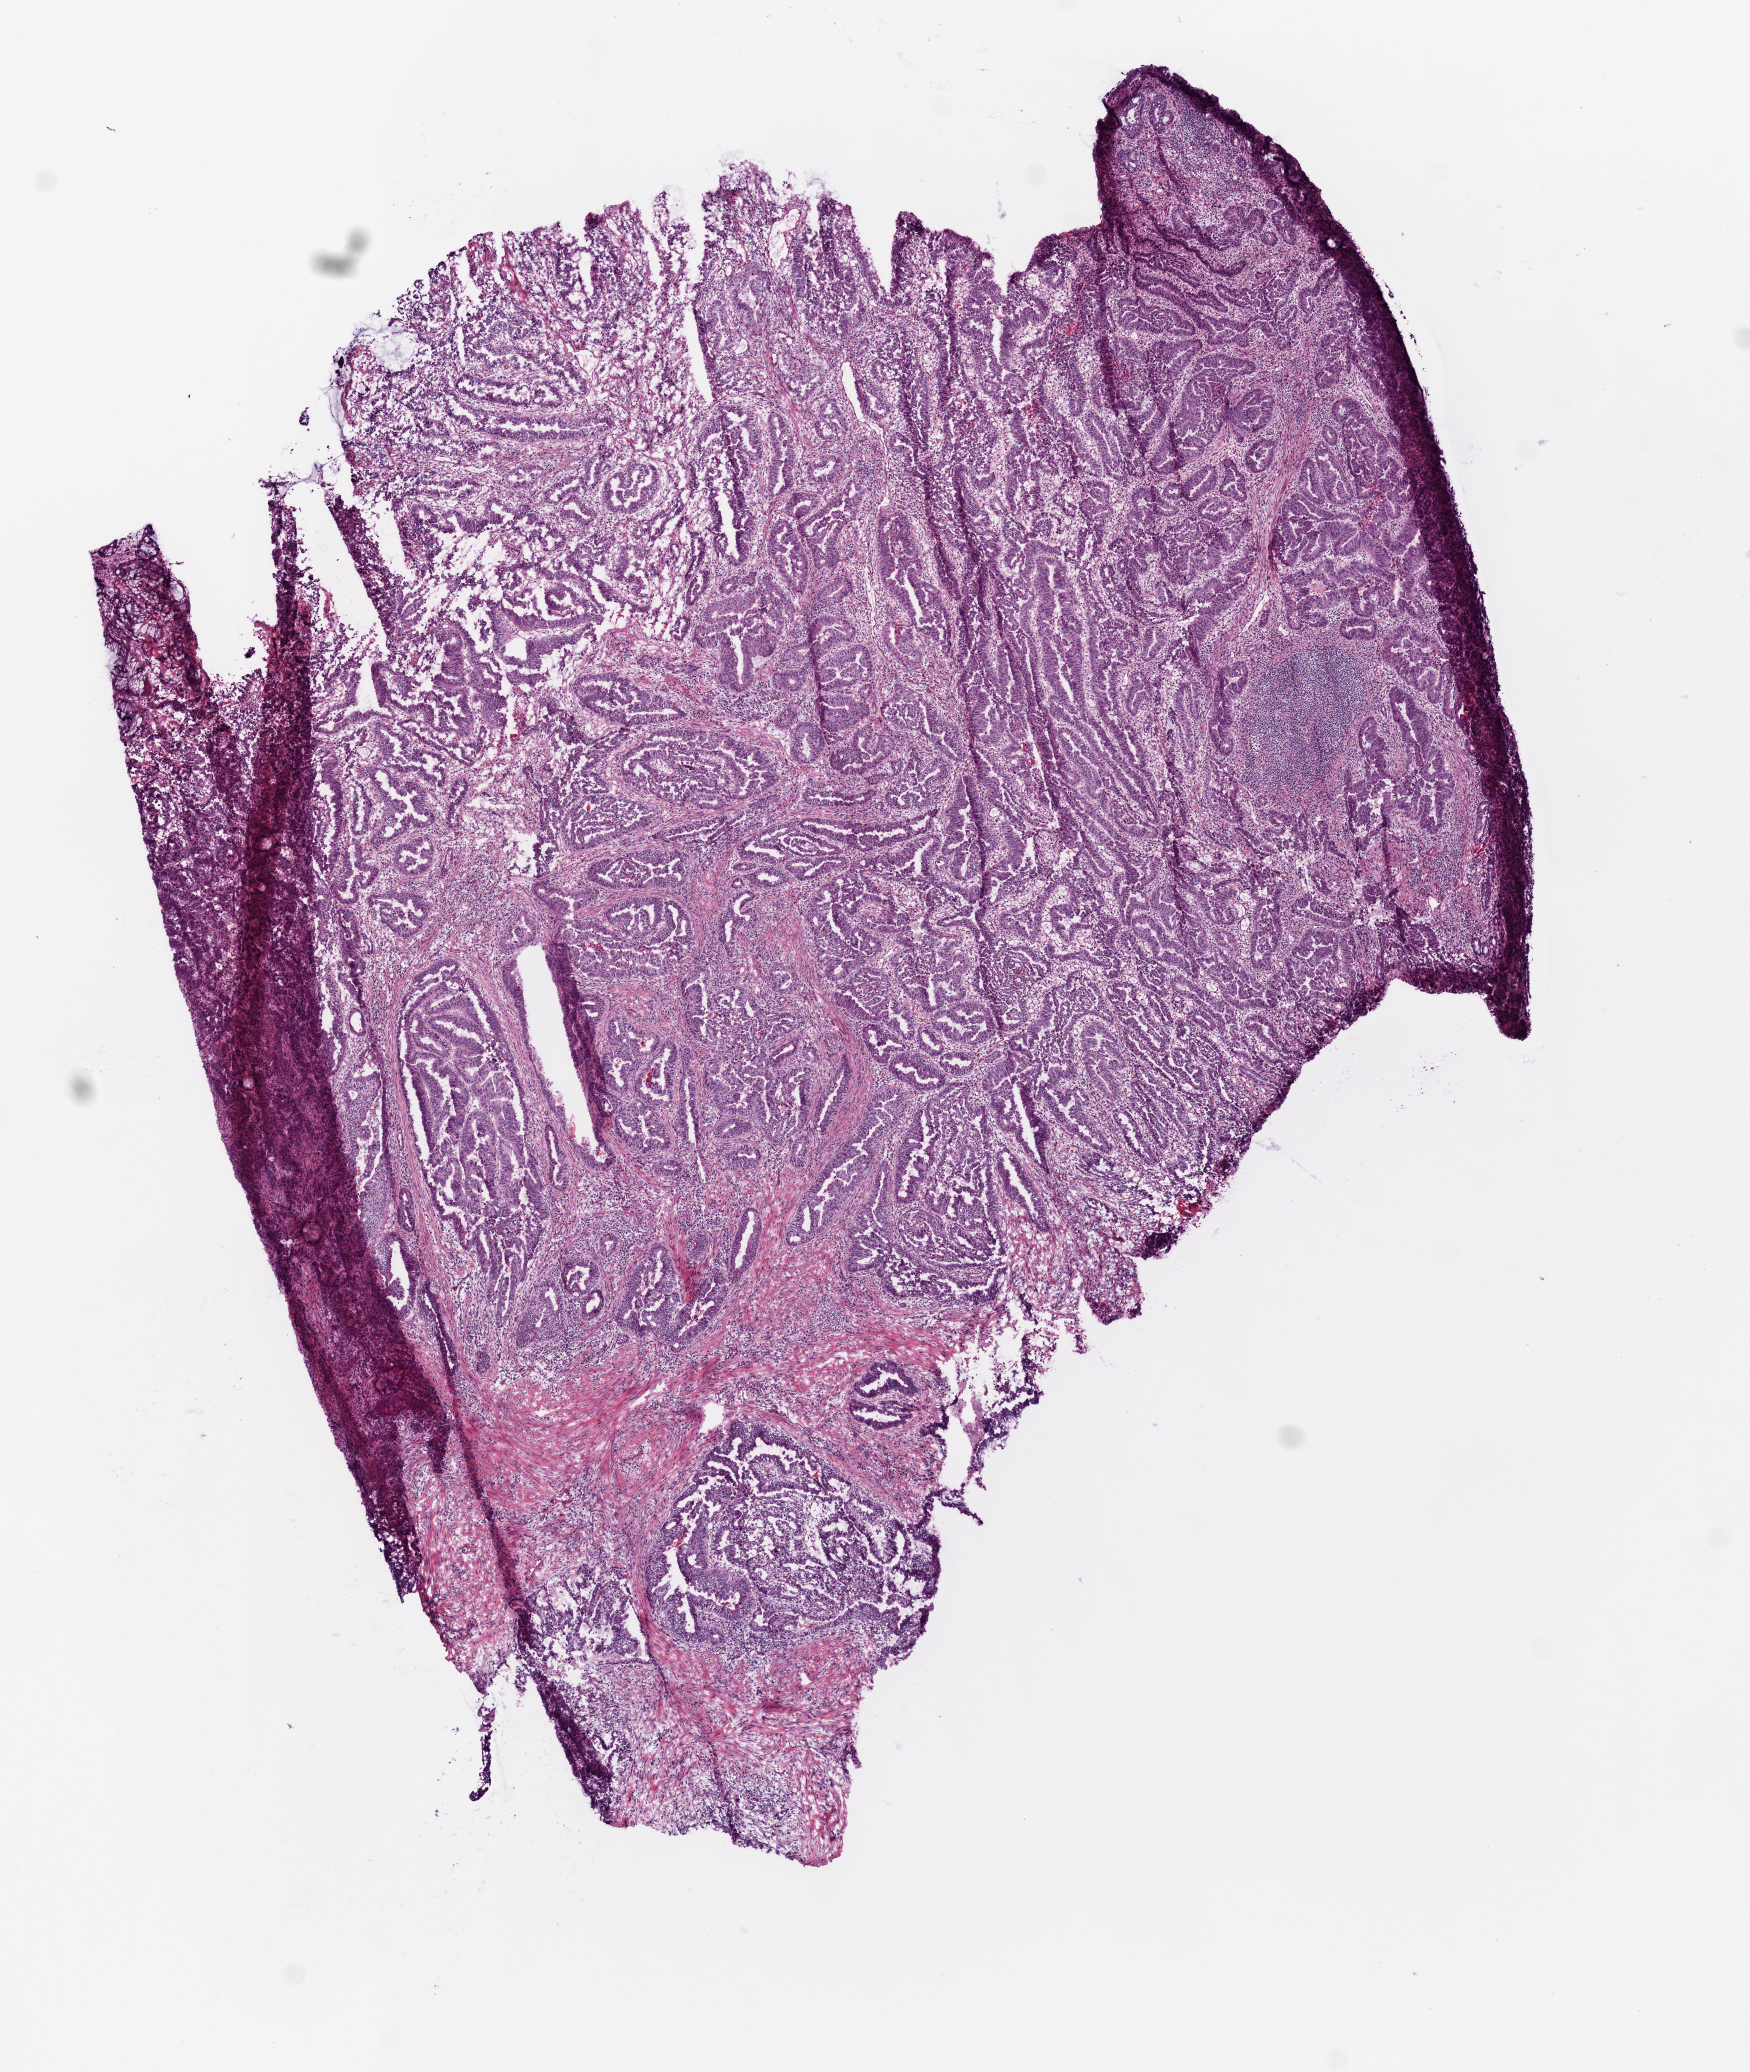
H&E whole-slide image, whole scanned area (about 7.0 x 8.3 mm, acquisition: 20x scan) shown as a low-resolution overview. Frozen section from the top of the tissue portion. Primary tumour sample from the rectum. Female, age 55 years at initial diagnosis. Pathologist review of this section (percent, as recorded): tumour cells 85%, tumour nuclei 88%, normal cells 0%, stromal cells 15%, necrosis 0%.
TNM: T3 N1 M0. AJCC pathologic stage: IIIB. Lymph nodes positive (case pathology): 1 of 32 examined. Diagnosis: Adenocarcinoma, NOS.